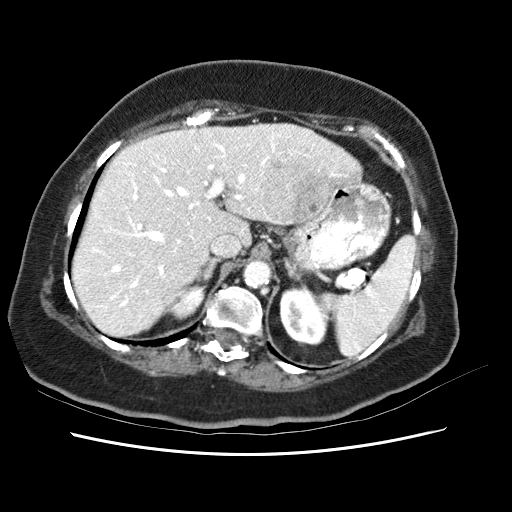
Contrast-enhanced abdominal CT (liver protocol), one axial slice; position 43 of 62 along the scan axis; reconstruction kernel STANDARD; soft-tissue window (W 400 / L 40 HU); 512 × 512 image matrix, field of view 340 × 340 mm. Case-level facts recorded for this patient, not image findings: diagnosis: hepatocellular carcinoma (patient treated with transarterial chemoembolisation; whether this scan precedes or follows treatment is not stated here); TNM stage (as recorded): Stage-I; Child-Pugh class: B.
Outlined on this slice (semi-automatically segmented with operator editing):
- liver parenchyma outside the tumour (the mass and vessels are separate outlines, so this box may not span the whole liver): bounding box <76,122,360,332> (left, top, right, bottom; pixels)
- mass: <257,144,331,222>
- liver vessels: <96,137,346,307>